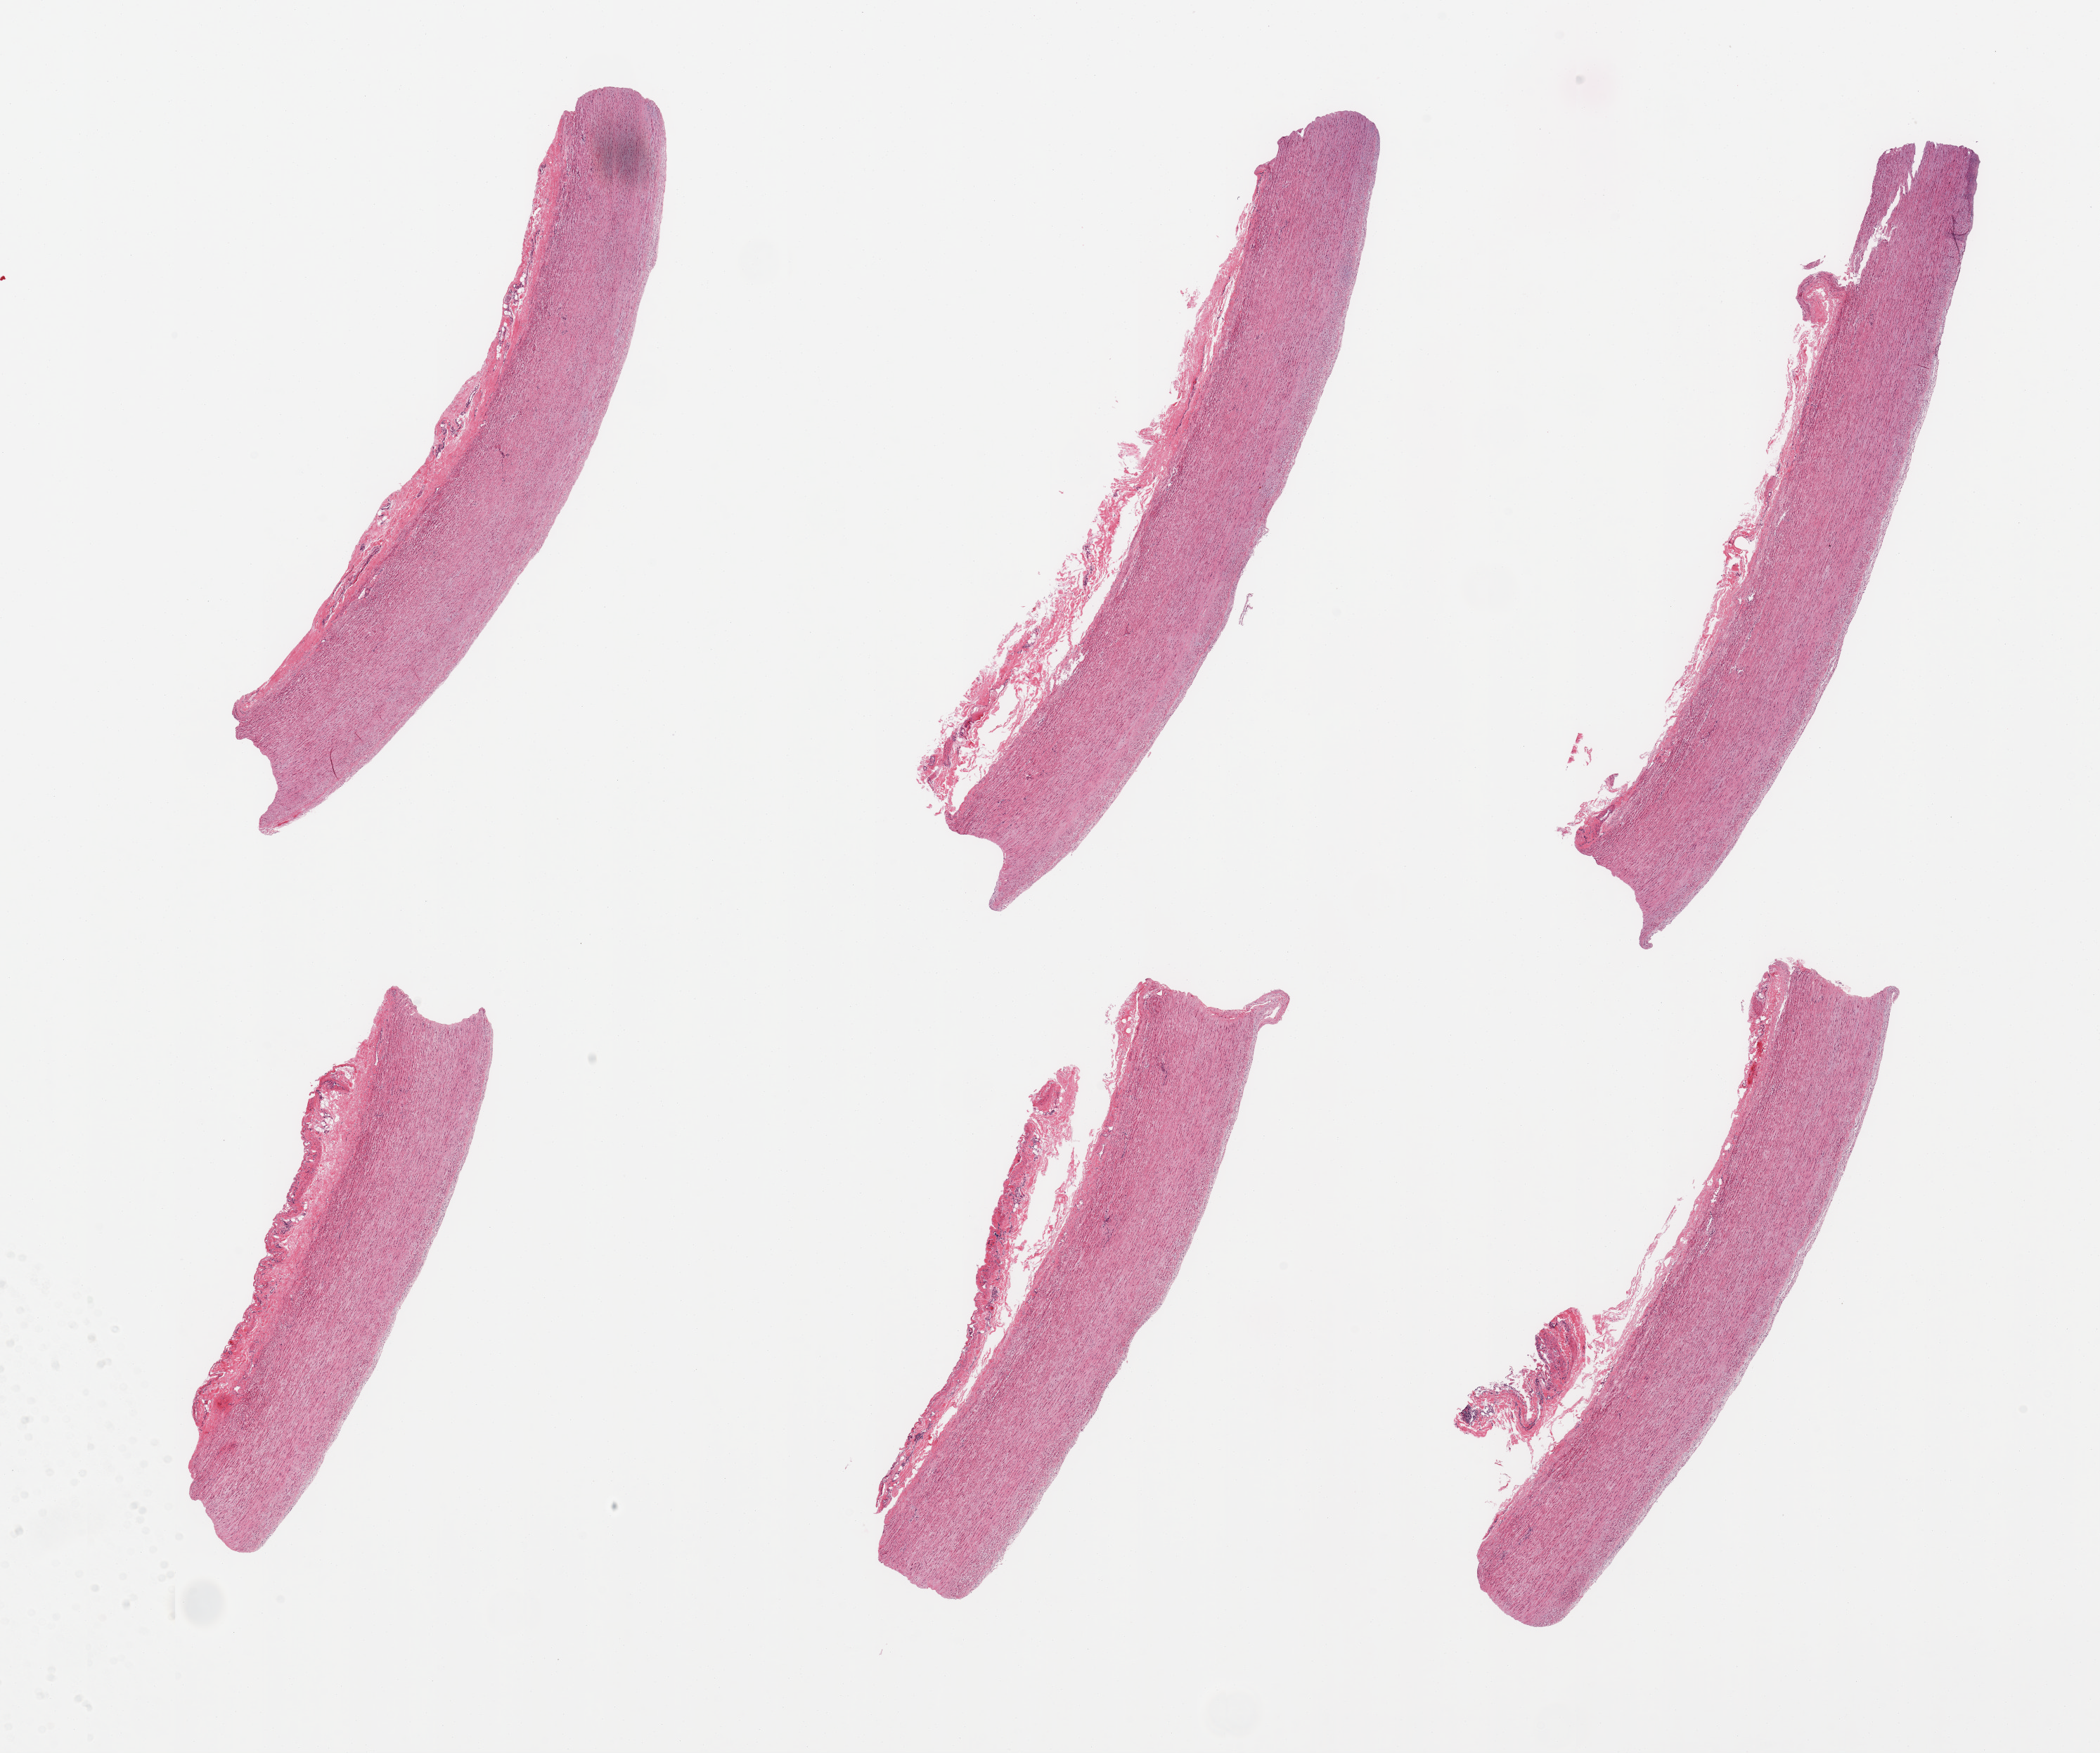
Whole-slide image, H&E stain, low-resolution overview of the scanned area, about 23.6 x 19.7 mm (acquisition: 20x scan); PAXgene-fixed paraffin-embedded (PFPE) section; target tissue: aorta; donor tissue sample. Donor: female.
- review note (as recorded): 6 pieces; no plaques; loose adventitia focally